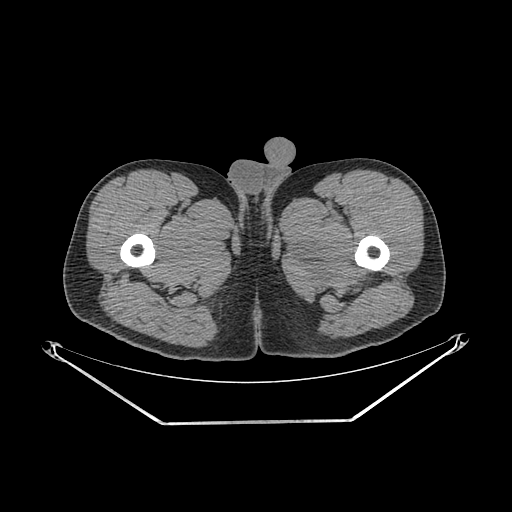
CT of an extremity soft-tissue mass (from a PET/CT study), one axial slice. Soft-tissue window (W 400 / L 40 HU). 3.75 mm slice thickness. 512 × 512 image matrix. Male patient. Case-level facts recorded for this patient, not image findings: histological type: extraskeletal osteosarcoma; grade: high; site of the primary tumour: left adductur.
Annotated regions visible in this slice (expert contour drawn on MRI and transferred to this co-registered scan by the dataset authors):
- gross tumour volume (mass): box from (x=283, y=199) to (x=387, y=300) px